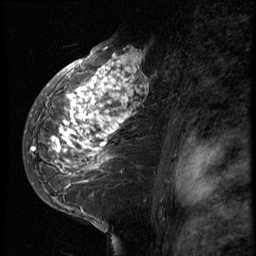
Breast MRI (dynamic contrast-enhanced), one sagittal slice; position 44 of 66 along the scan axis; 3 images stored at this slice position (order not interpretable as contrast timing); 1.5 T; TE 4.2 ms, TR 8.9 ms; 256 × 256 image matrix, field of view 200 × 200 mm. Female patient, age 39 years. From the clinical record (not read from this slice): setting: breast cancer imaged before/during neoadjuvant chemotherapy; receptor status: HER2-positive.
Structures marked on this image (semi-automatic segmentation, software-assisted and operator-edited):
- analysis volume of interest (the breast-tissue region the enhancement analysis was run in; not a lesion): box from (x=29, y=44) to (x=166, y=196) px
- tumour enhancement mask (voxels above the 140 % enhancement threshold inside the analysis volume of interest): (x=29, y=46)–(x=150, y=183)